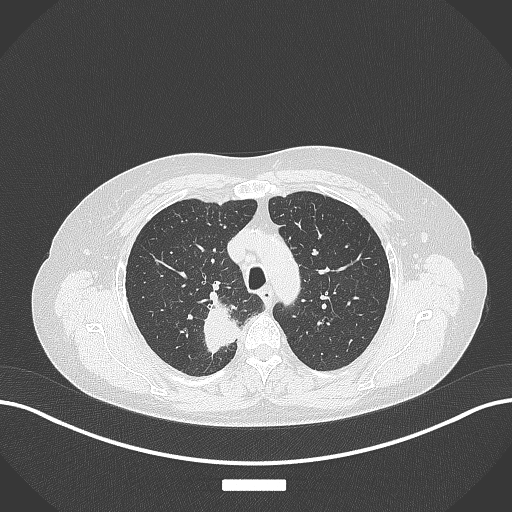
Chest CT, one axial slice; position 292 of 357 along the scan axis; 120 kVp; lung window (W 1500 / L -600 HU); 512 × 512 image matrix, field of view 400 × 400 mm. Patient: female, 62 years. Case-level facts recorded for this patient, not image findings: clinical TNM (as recorded): T1c N1 M0.
Structures marked on this image (rectangle marked by the reading radiologist):
- lung tumour (recorded histology: squamous cell carcinoma): bounding box [x1, y1, x2, y2] px = [195, 295, 237, 355]